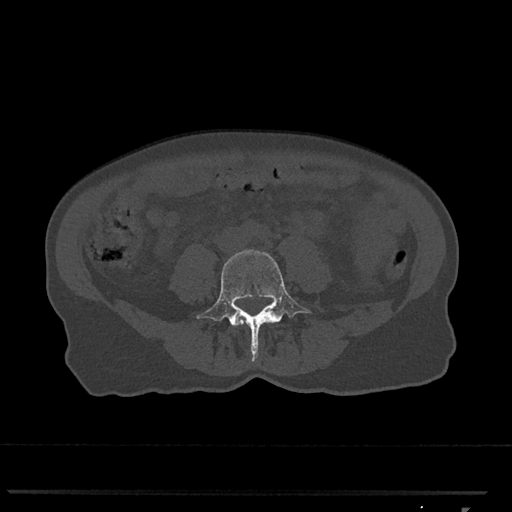
CT including the spine, one axial slice; slice 215 of 793 in the series (ordered by position); 120 kVp; bone window (W 1800 / L 400 HU); 512 × 512 image matrix, field of view 380 × 380 mm. Female patient, age 62 years. Case-level facts recorded for this patient, not image findings: primary cancer: renal.
Outlined on this slice (semi-automatic segmentation, software-assisted and operator-edited):
- L4 vertebra: bounding box [x1, y1, x2, y2] px = [196, 250, 311, 361]